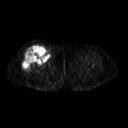
FDG PET of an extremity soft-tissue mass (from a PET/CT study), one axial slice; slice 260 of 311 in the series (ordered by position); 128 × 128 image matrix. Female patient, age 57 years. Case-level facts recorded for this patient, not image findings: histological type: pleiomorphic undifferentiated sarcoma; grade: high; site of the primary tumour: right quadricep.
Outlined on this slice (expert contour drawn on MRI and transferred to this co-registered scan by the dataset authors):
- tumour plus oedema (research contour): bounding box [x1, y1, x2, y2] px = [22, 46, 49, 71]
- tumour (research contour): [22, 46, 49, 71]